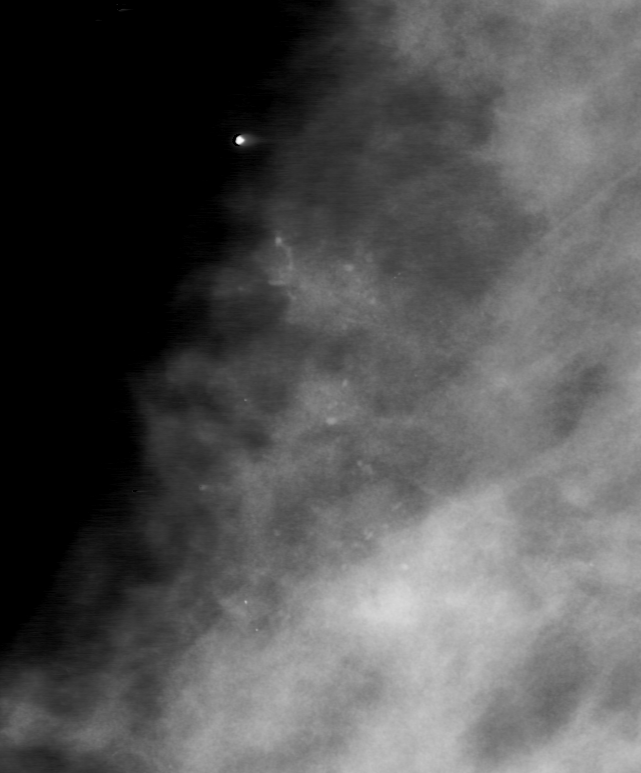
Cropped region of a digitized screen-film mammogram centred on a radiologist-marked abnormality; right breast; MLO view.
Calcifications, morphology punctate / fine linear branching, distribution clustered; BI-RADS assessment category 0; subtlety rating 5 on a 1 (subtle) to 5 (obvious) scale; pathology (as recorded): malignant.